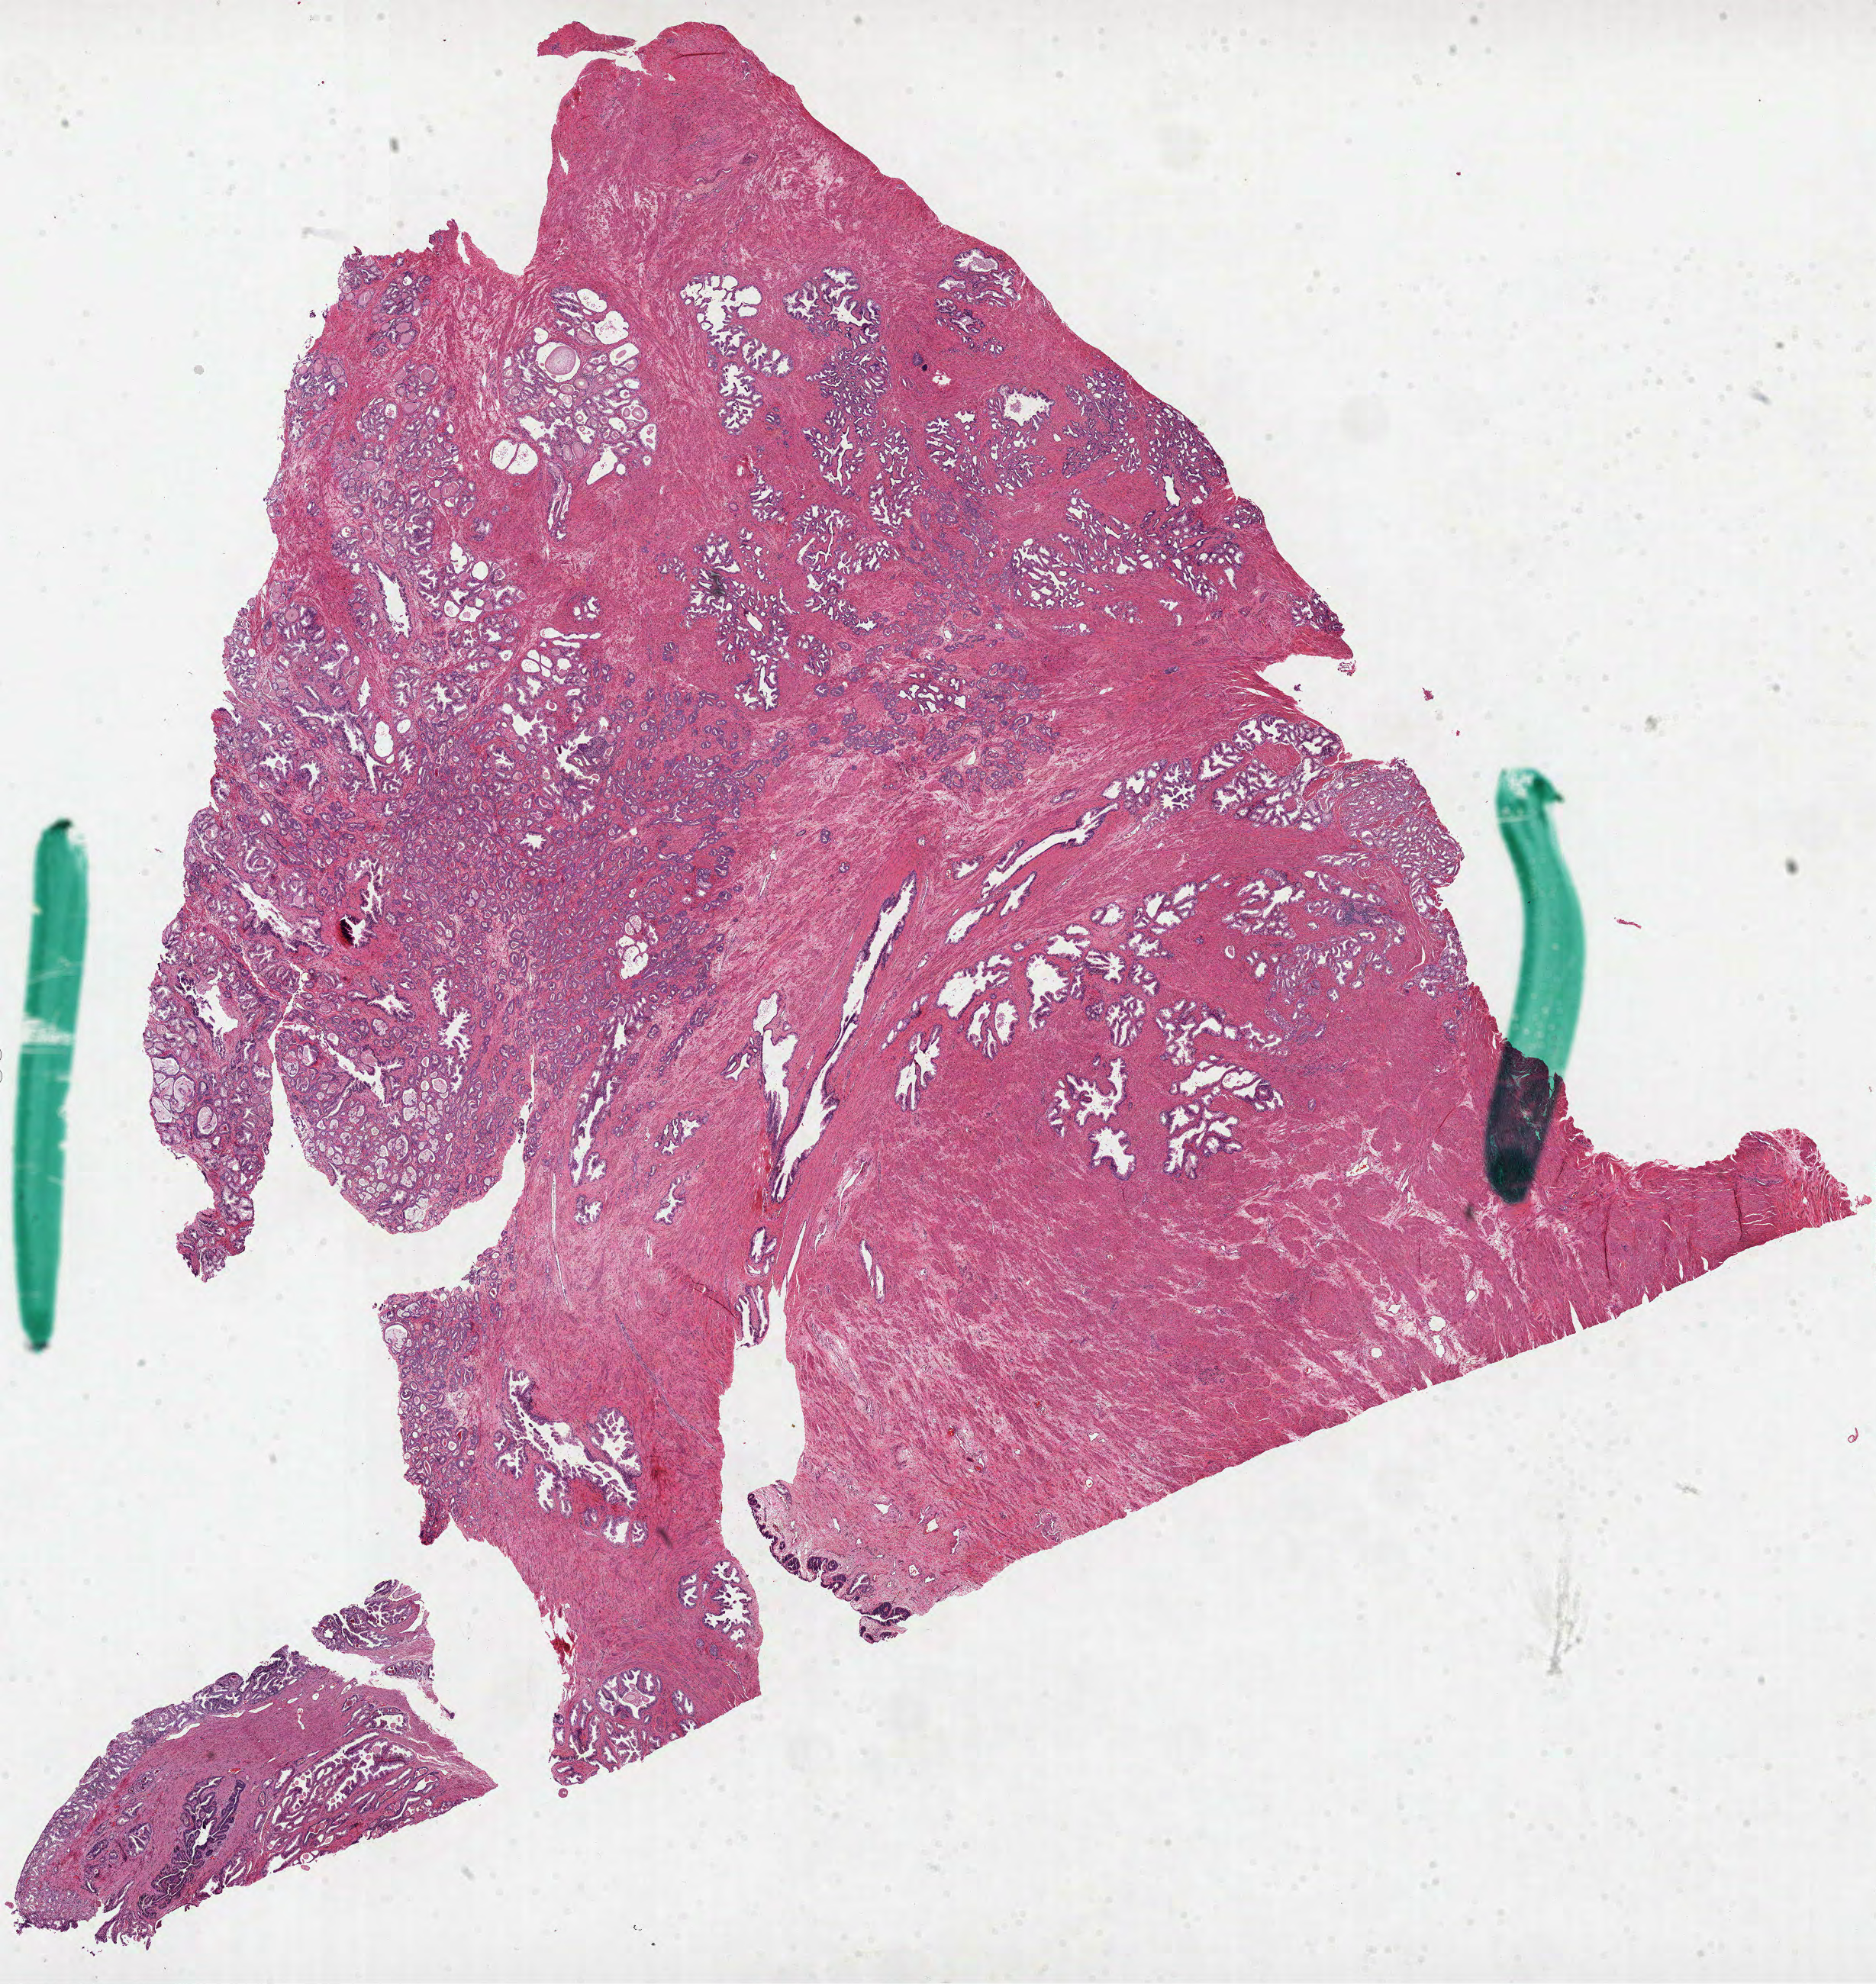
Whole-slide histology image, H&E, low-resolution overview of the scanned area, about 19.8 x 21.0 mm. Formalin-fixed paraffin-embedded (FFPE) diagnostic section. Sample: primary tumour, prostate. Male patient; age at initial diagnosis 46 years.
Diagnosis: Acinar cell carcinoma (prostate gland).